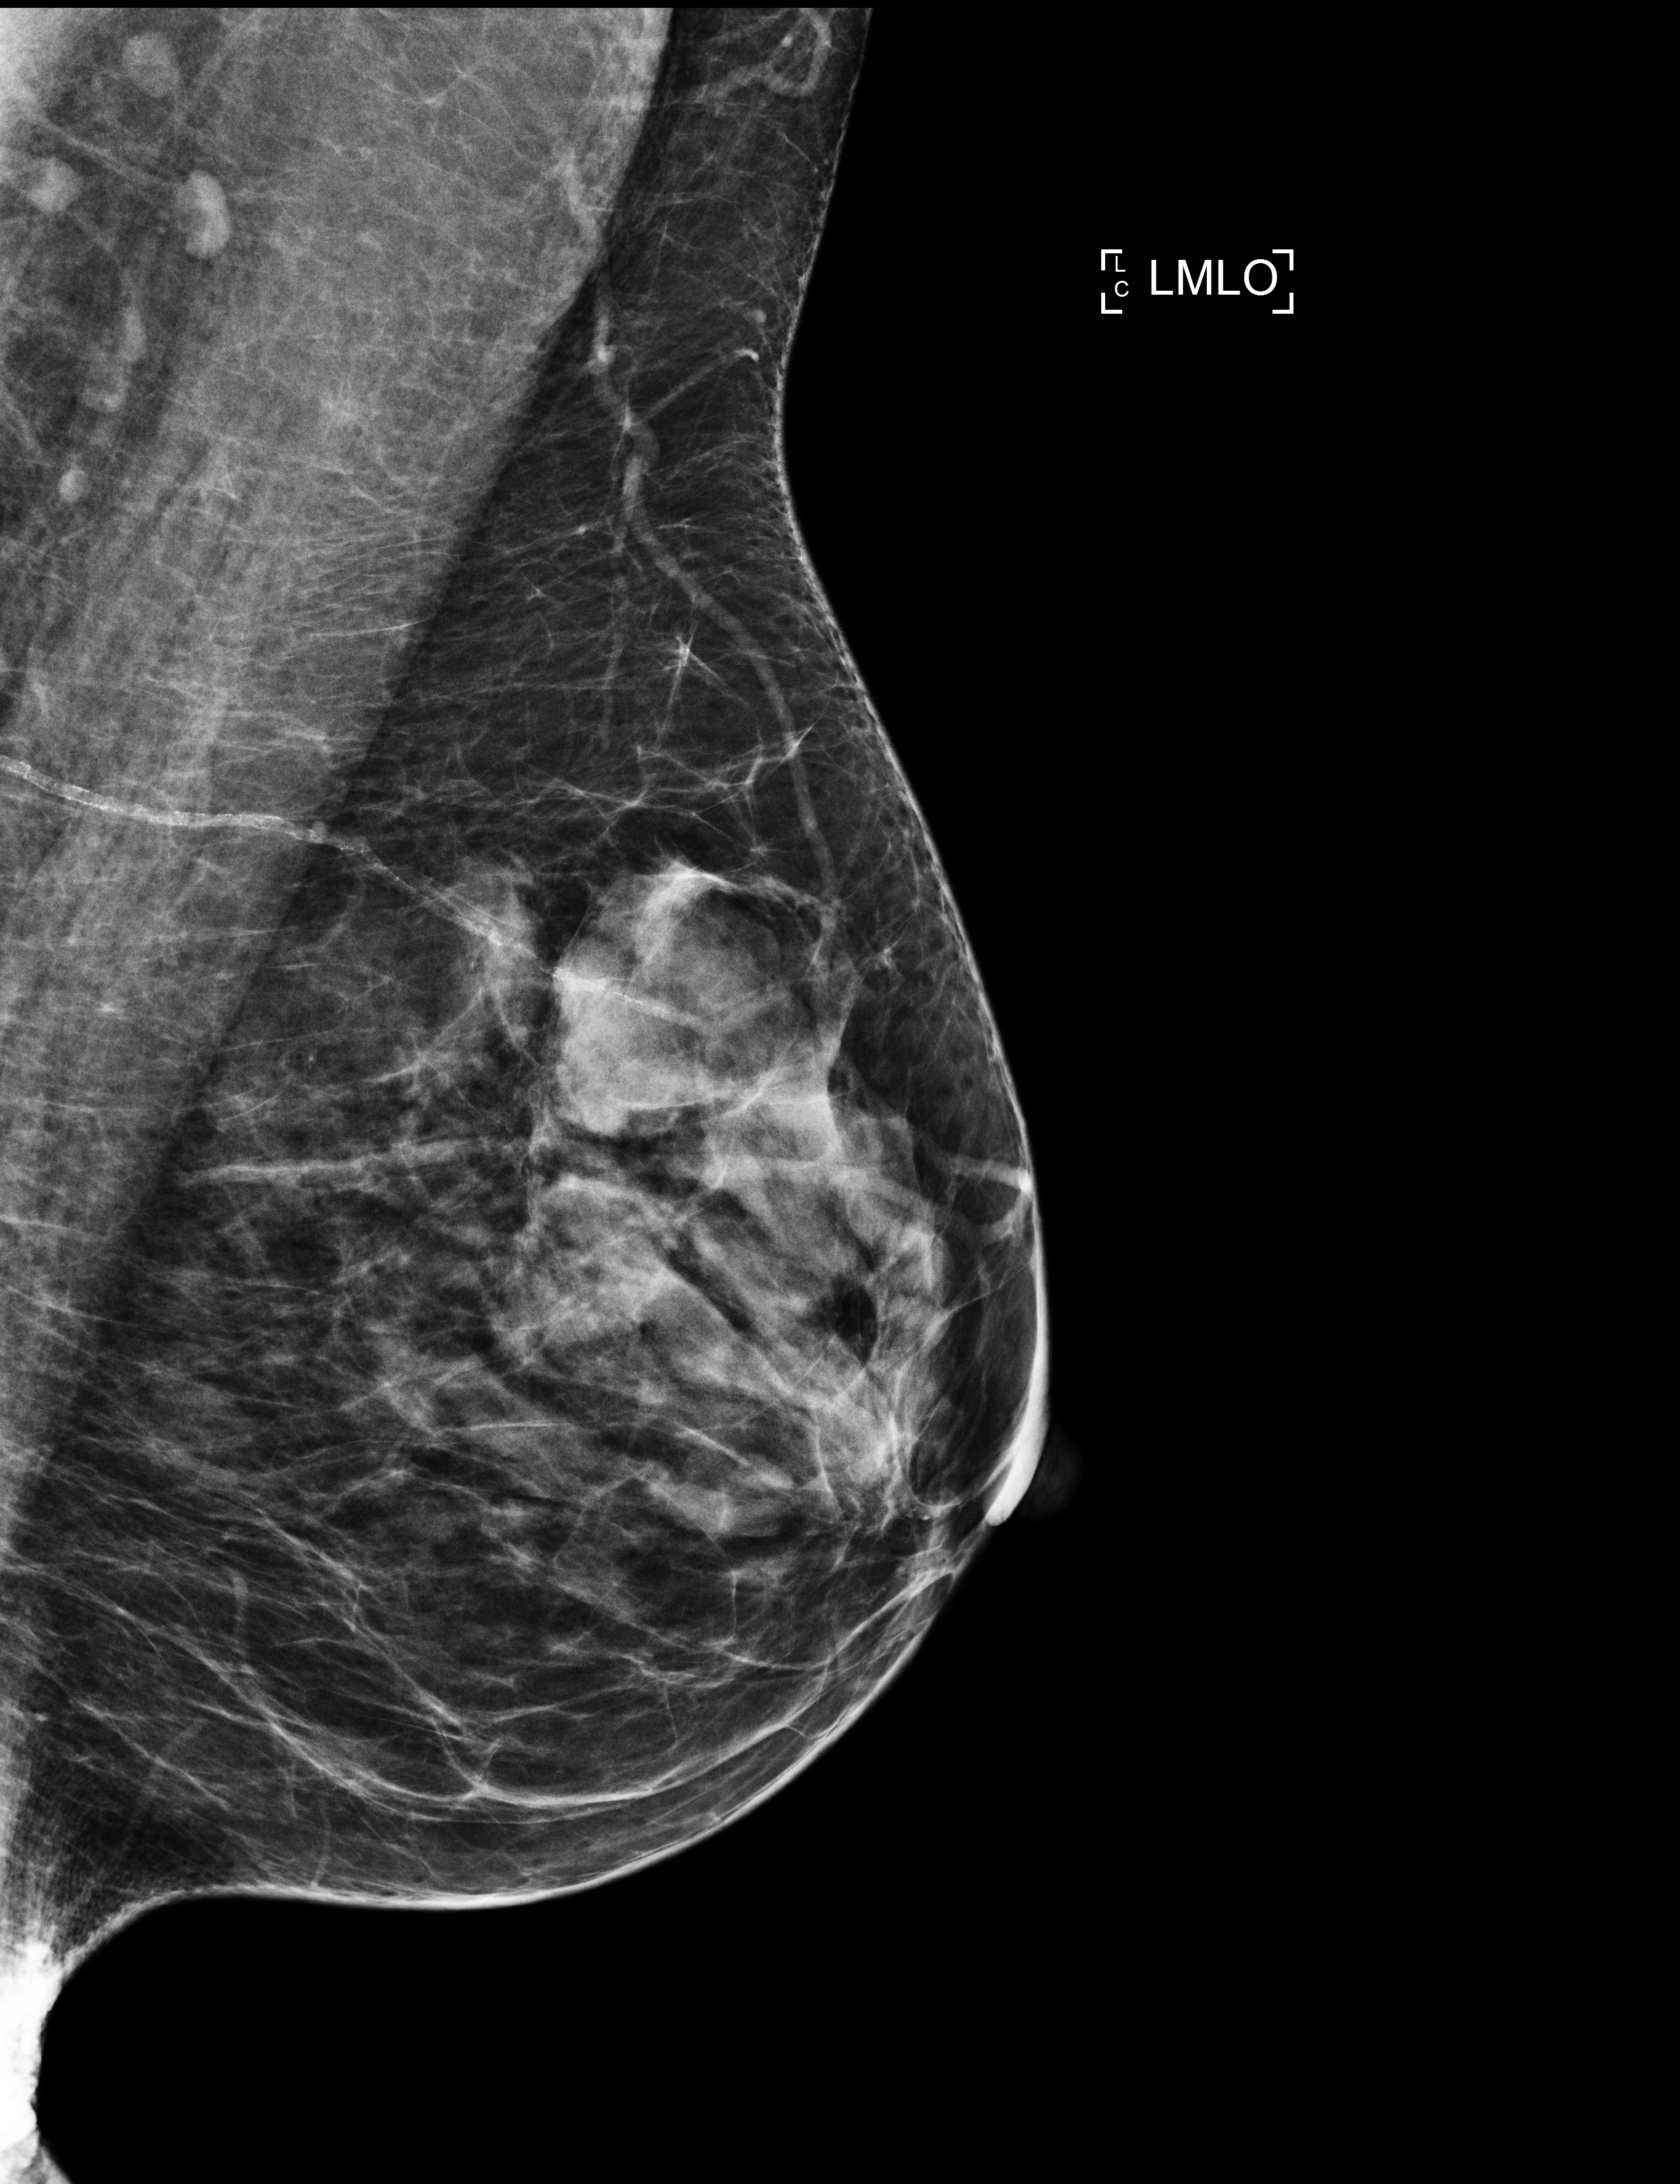
Full-field digital mammogram (FFDM); left breast; medio-lateral oblique projection; screening examination. Patient: female, 57 years.
- BI-RADS breast density category at the screening exam (both breasts, scale 1–4): 3
- final BI-RADS assessment for this screening round (tomosynthesis exam, both breasts): category 1
- recall: no recall after this screen